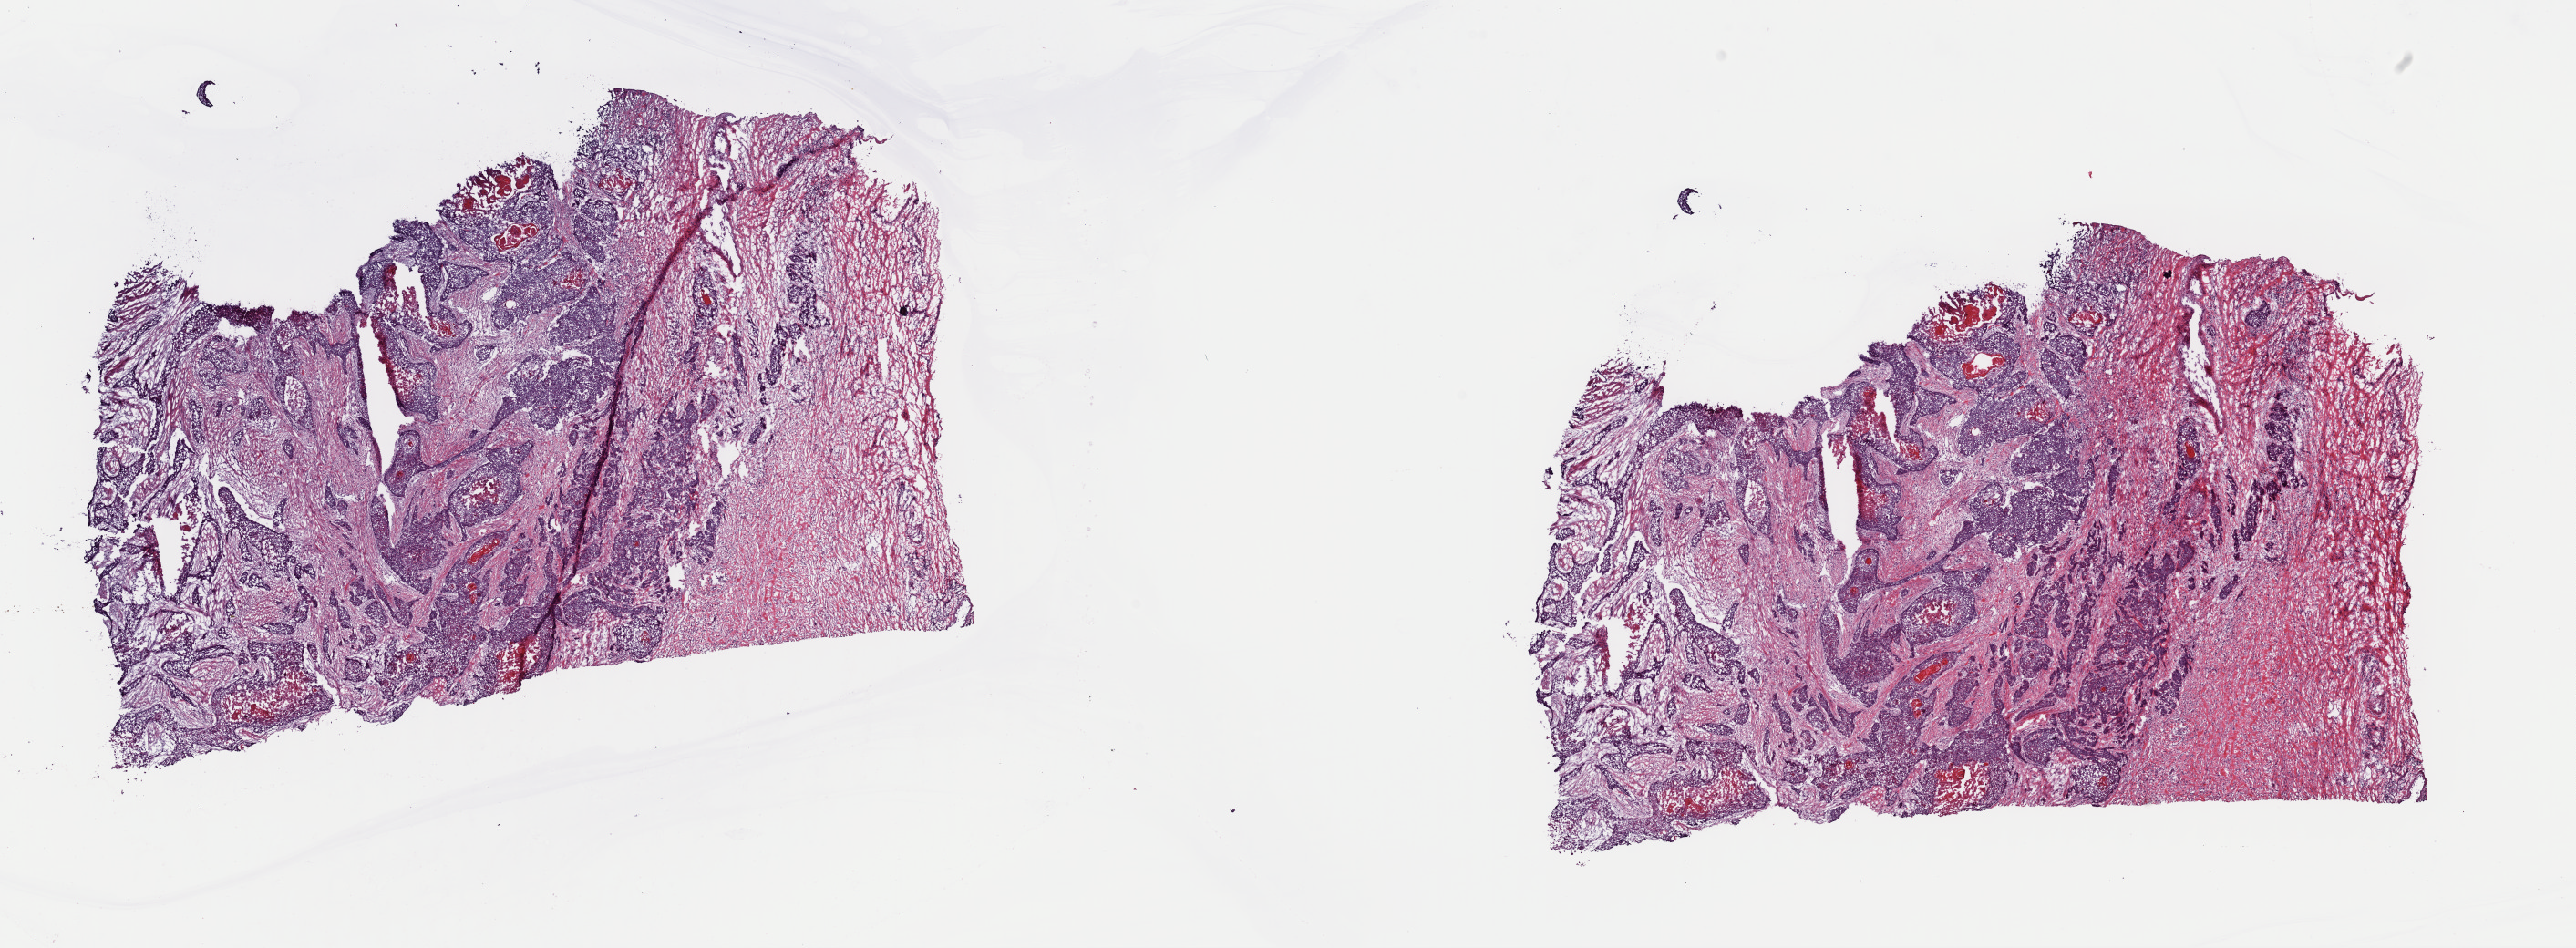
Whole-slide histology image, H&E, shown as a low-resolution overview of the whole scanned area (about 22.3 x 8.2 mm, acquisition: 40x scan); frozen section from the top of the tissue portion; sample: primary tumour, esophagus. Patient: male, age at initial diagnosis 54 years. Histologic grade: G2 (moderately differentiated). Slide review estimates, as recorded: tumour cells 40%, tumour nuclei 80%, normal cells 0%, stromal cells 55%, necrosis 5%. Inflammatory infiltration, as recorded: lymphocyte infiltration 4%, monocyte infiltration 2%, neutrophil infiltration 0%.
- histologic diagnosis: Squamous cell carcinoma, NOS (lower third of esophagus)
- AJCC pathologic stage: IIB (6th edition)